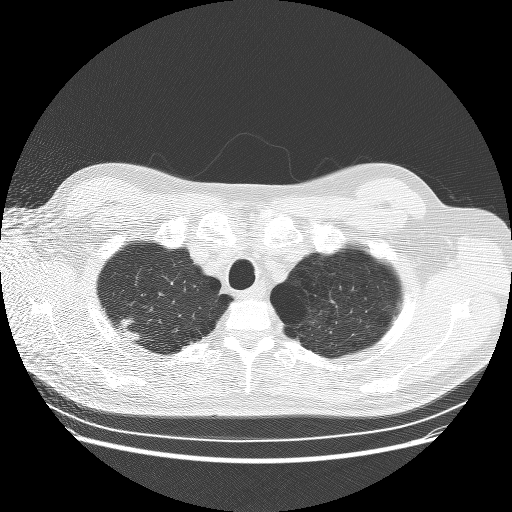
Low-dose screening chest CT, one axial slice. Reconstruction kernel BONE. 120 kVp. Lung window (W 1500 / L -600 HU). 2.5 mm slice thickness. 512 × 512 image matrix, field of view 370 × 370 mm.
Outlined on this slice (outlined manually by an expert reader):
- lesion 1 (tumor, upper lobe of right lung): bounding box [x1, y1, x2, y2] px = [121, 319, 140, 340]